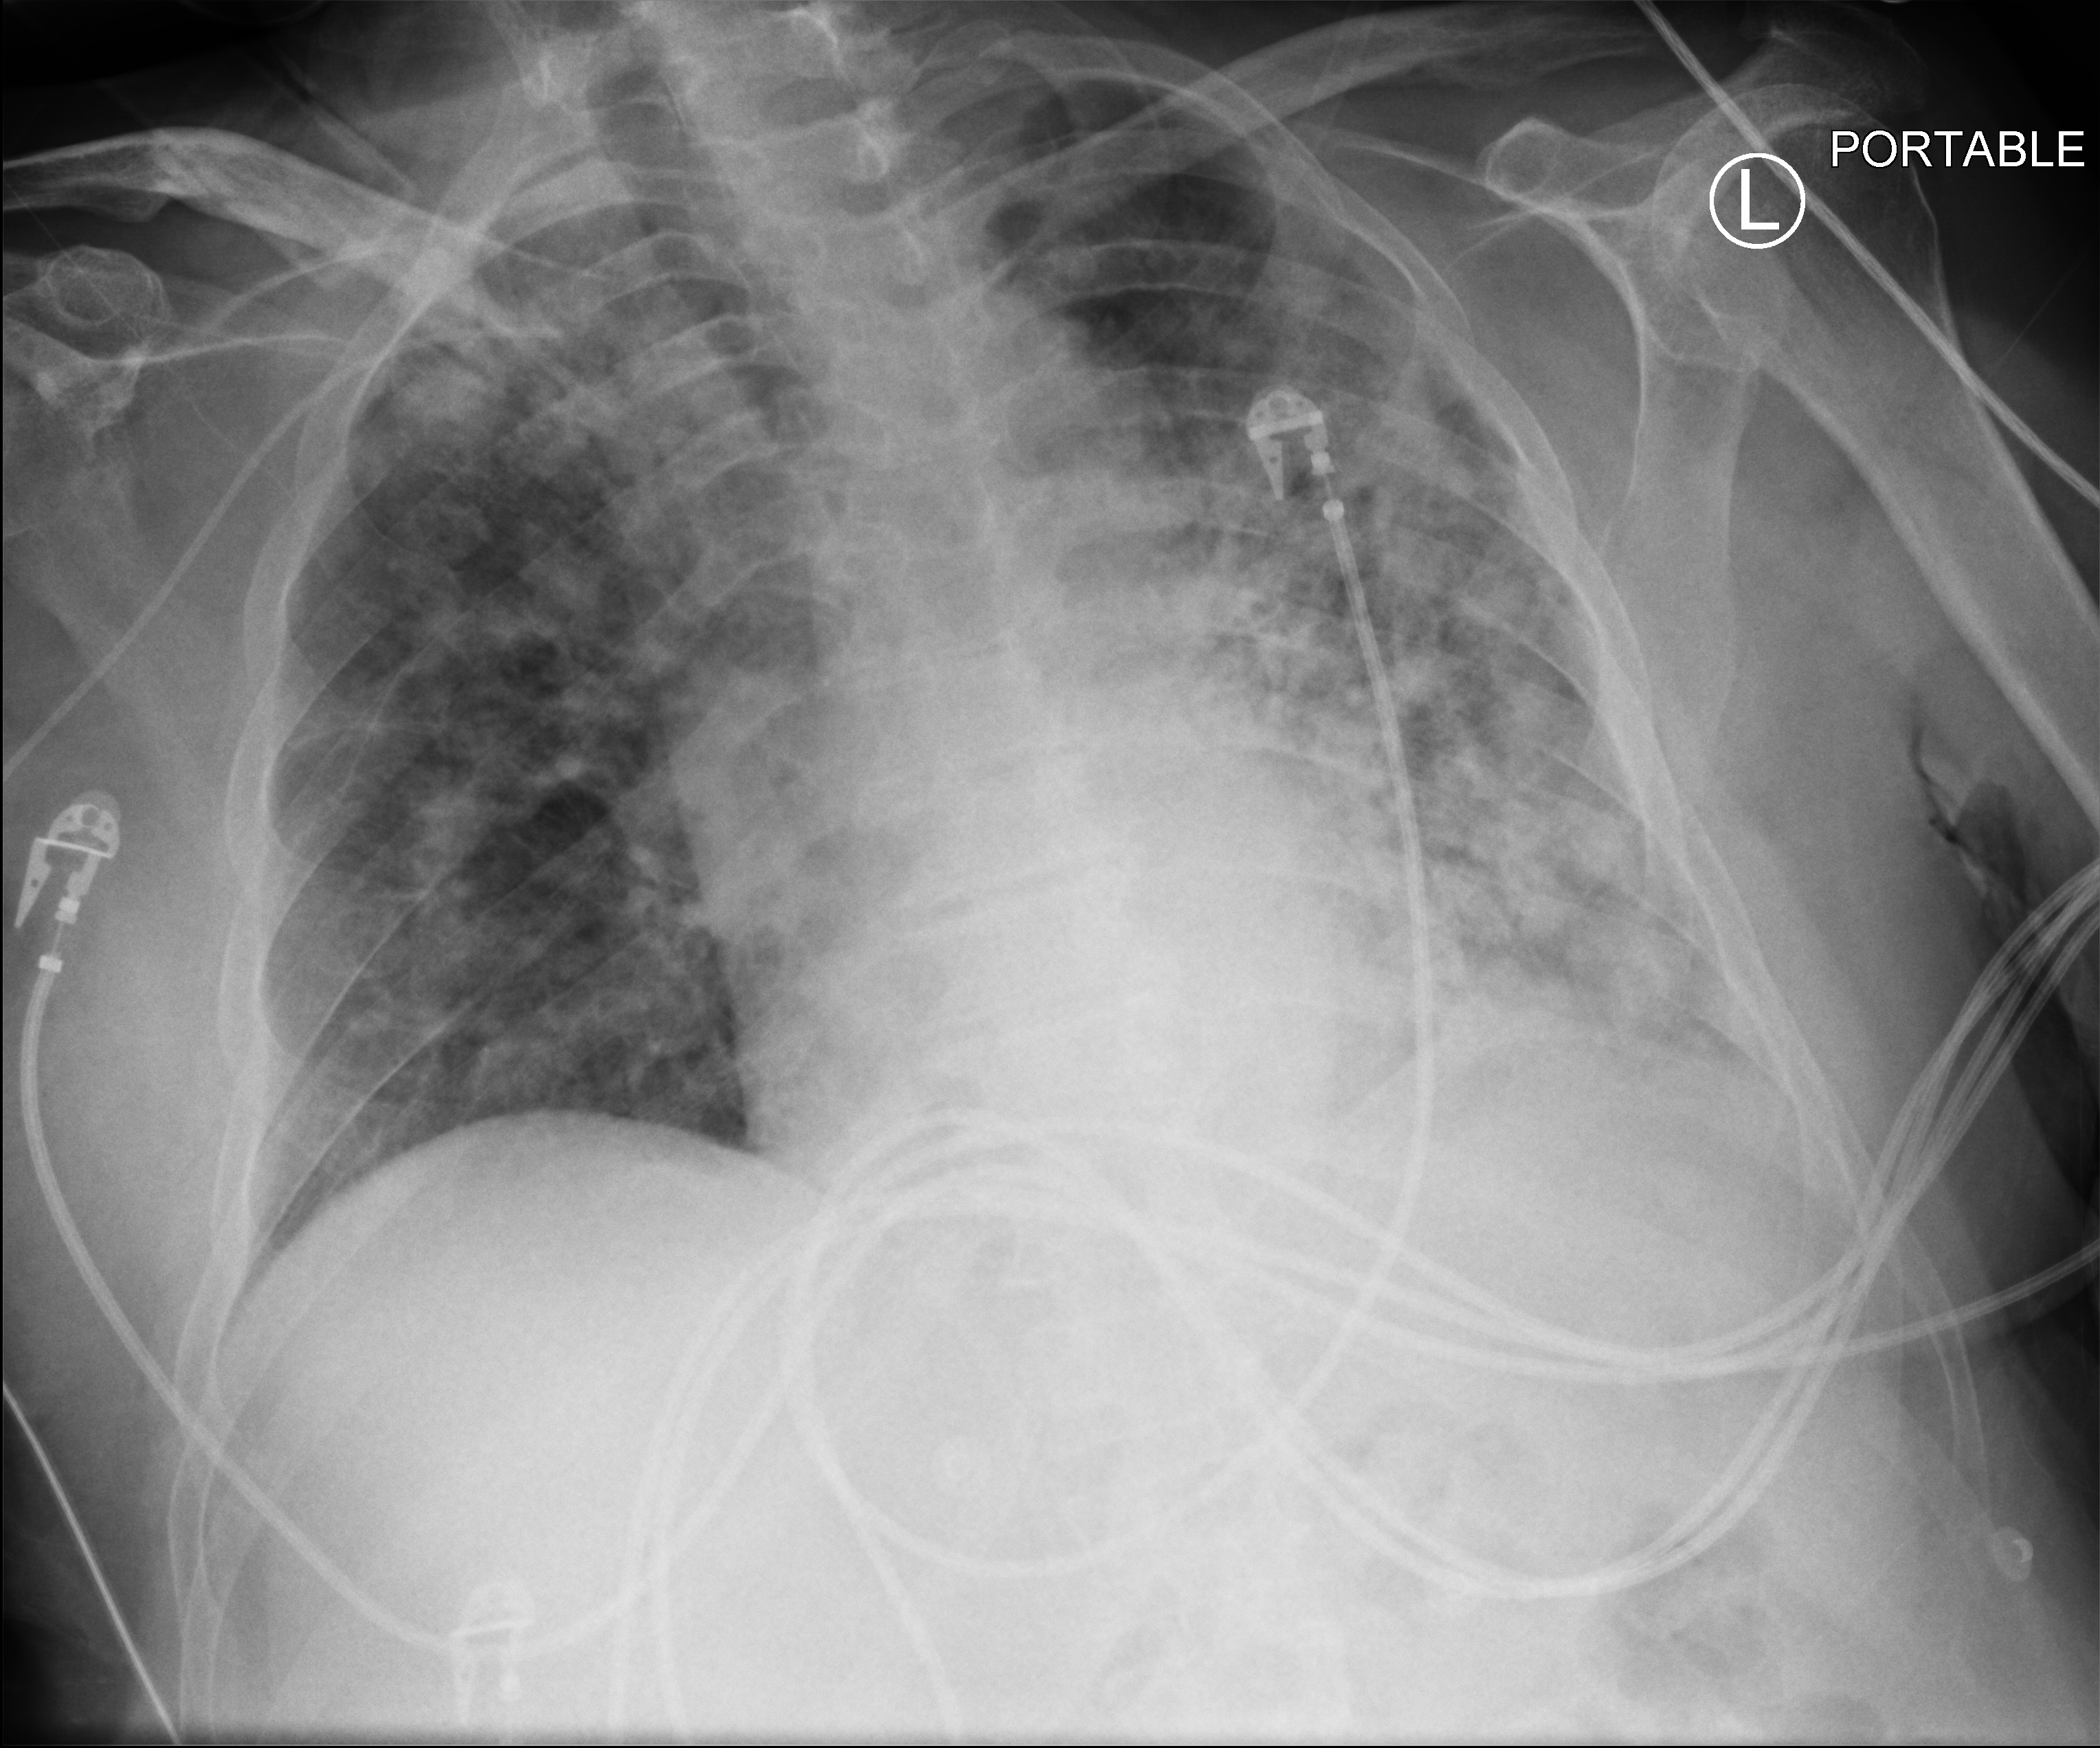
Chest X-ray (portable), anteroposterior (AP) projection. Male patient hospitalised with COVID-19, age 60–74 years.
Hospital-stay facts (about this admission, not read from this image; timing relative to this image not recorded): other chronic lung disease (admission record): no.